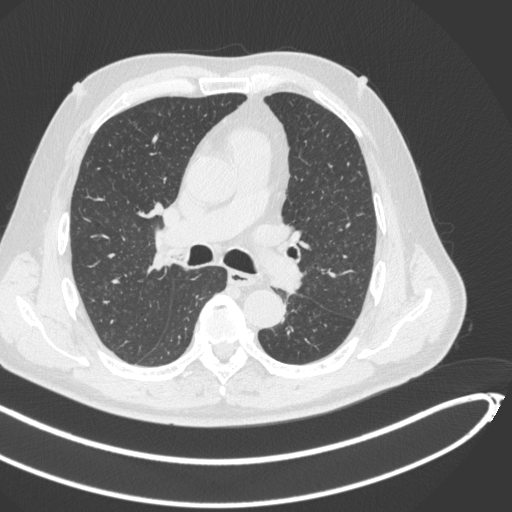
Chest CT, one axial slice. Position 280 of 466 along the scan axis. 120 kVp. Lung window (W 1500 / L -600 HU). 512 × 512 image matrix. Male patient, age 64 years. Case-level facts recorded for this patient, not image findings: clinical TNM (as recorded): T1c N0 M0.
Outlined on this slice (rectangle marked by the reading radiologist):
- lung tumour (recorded histology: squamous cell carcinoma): box from (x=255, y=242) to (x=306, y=295) px